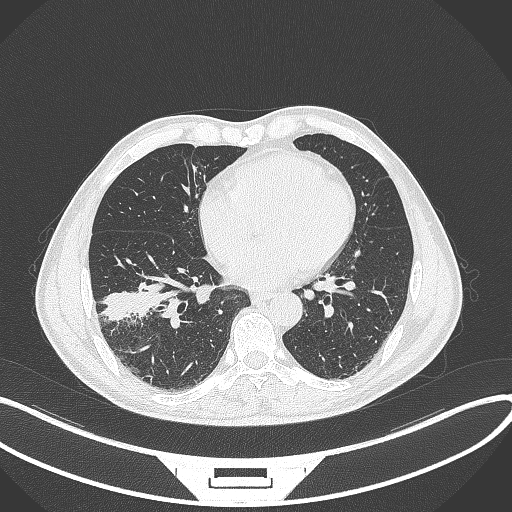
Chest CT, one axial slice. Reconstruction kernel B70f. 120 kVp. Lung window (W 1500 / L -600 HU). 1 mm slice thickness. 512 × 512 image matrix, field of view 400 × 400 mm. Male patient, age 58 years. Case-level facts recorded for this patient, not image findings: clinical TNM (as recorded): T3 N0 M0.
Annotated regions visible in this slice (bounding box drawn by a radiologist):
- lung tumour (recorded histology: squamous cell carcinoma): box from (x=98, y=287) to (x=164, y=318) px